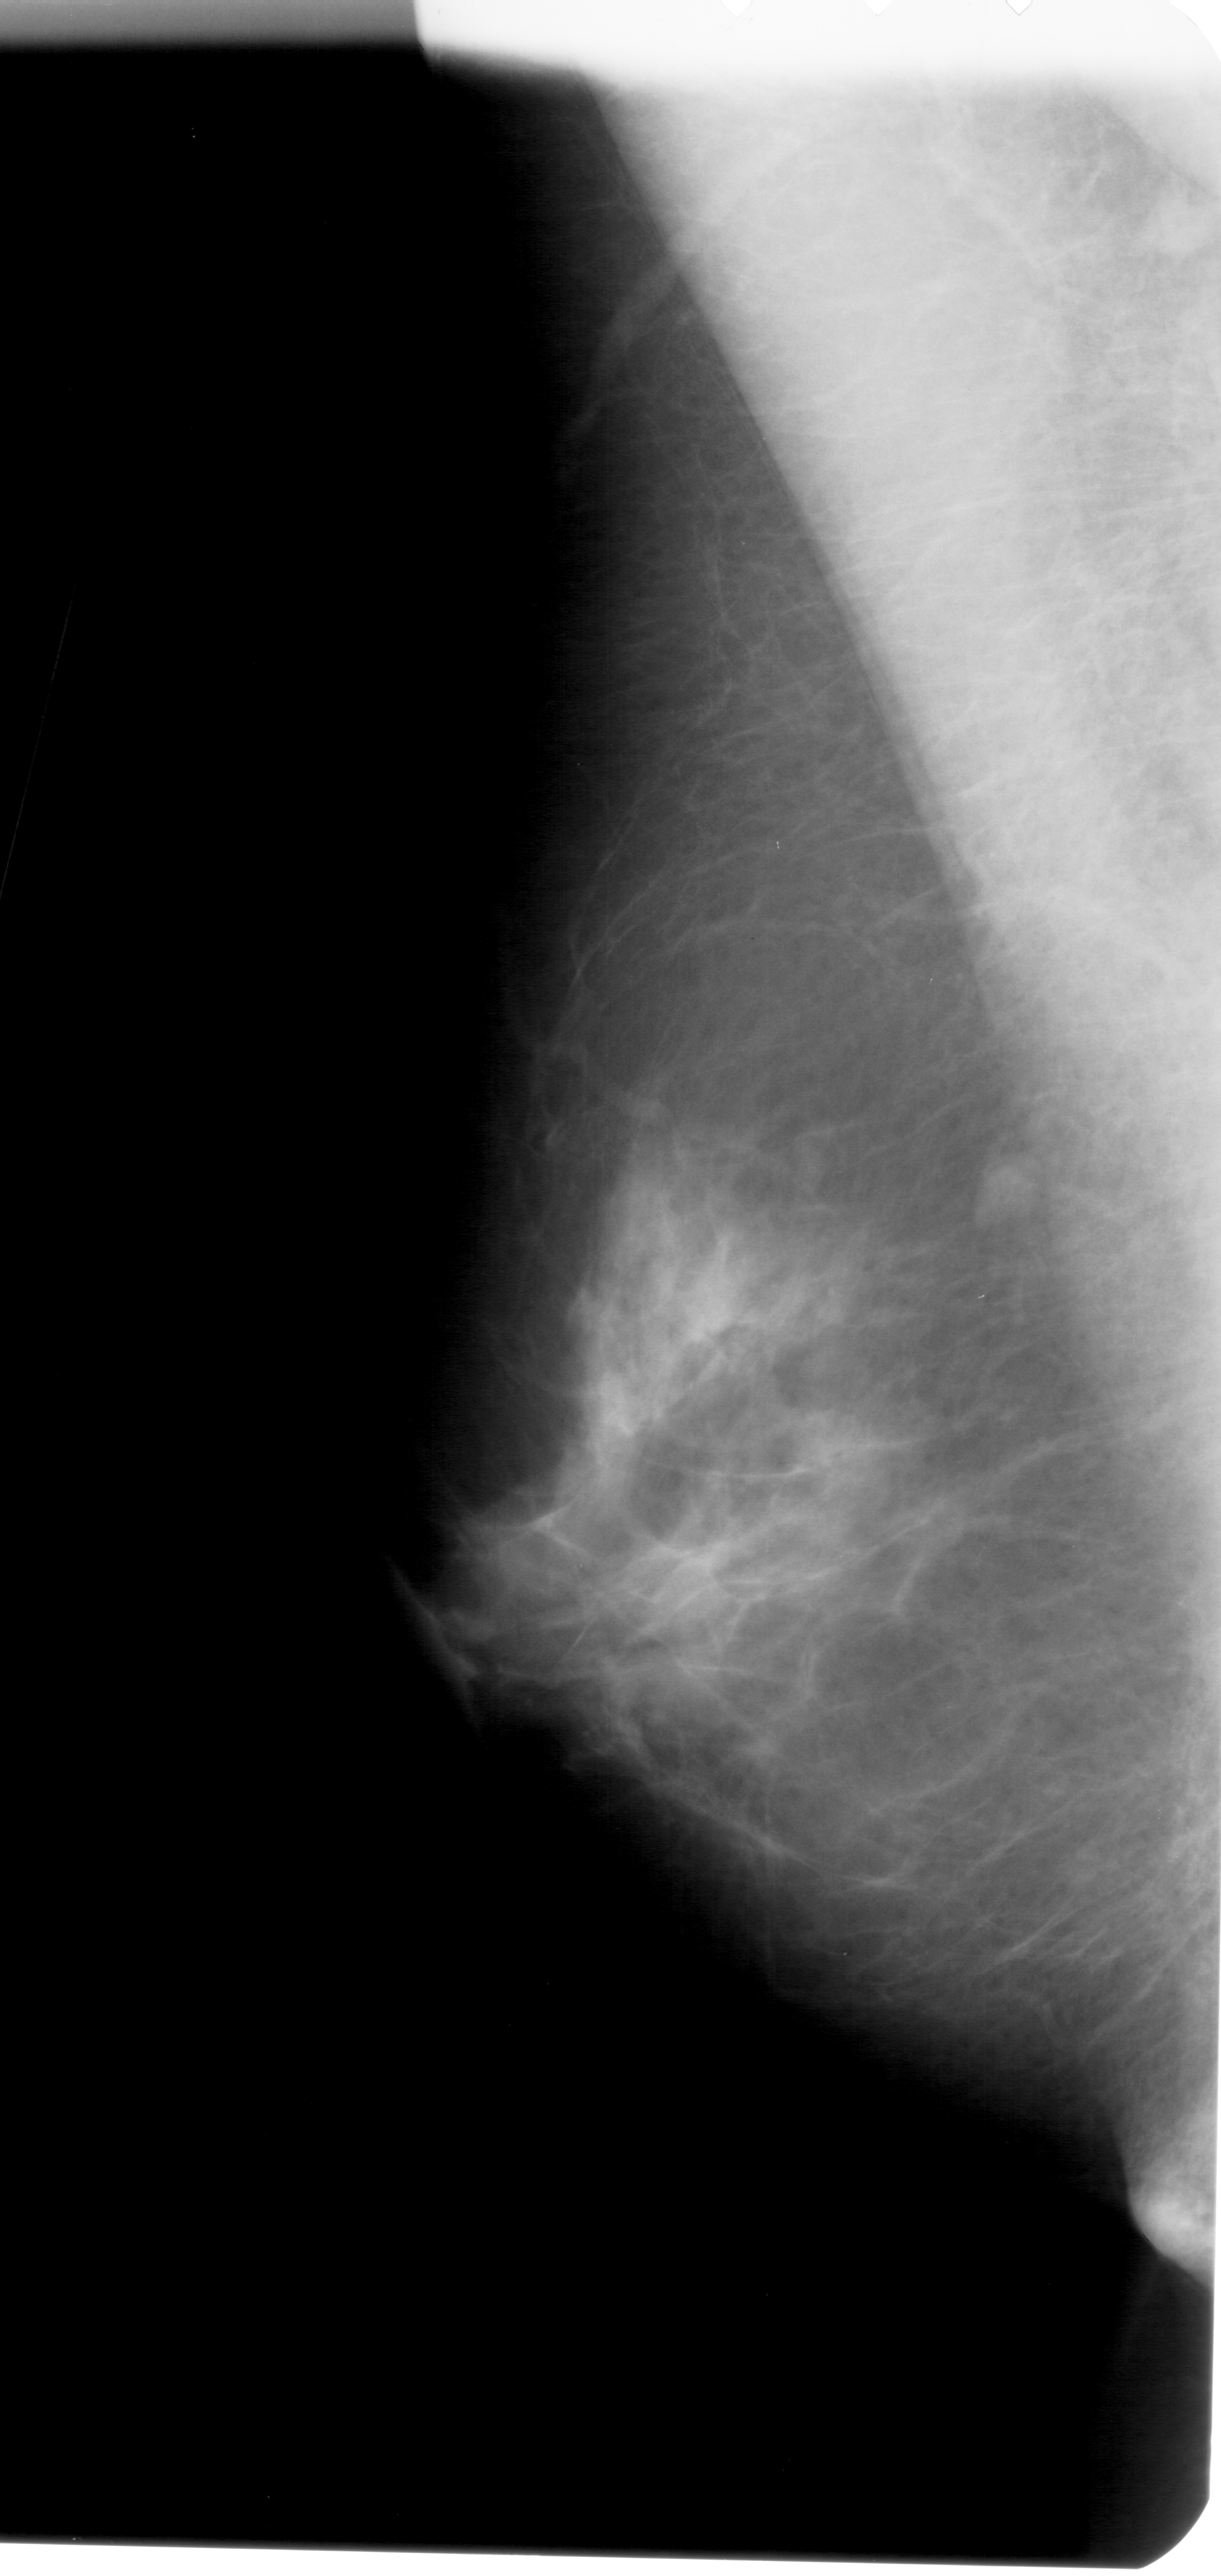
Mammogram (digitized film); left breast; MLO view.
Radiologist-marked abnormalities on this image: mass, shape oval, margins circumscribed; BI-RADS assessment category 3; subtlety rating 4 on a 1 (subtle) to 5 (obvious) scale; pathology (as recorded): benign.